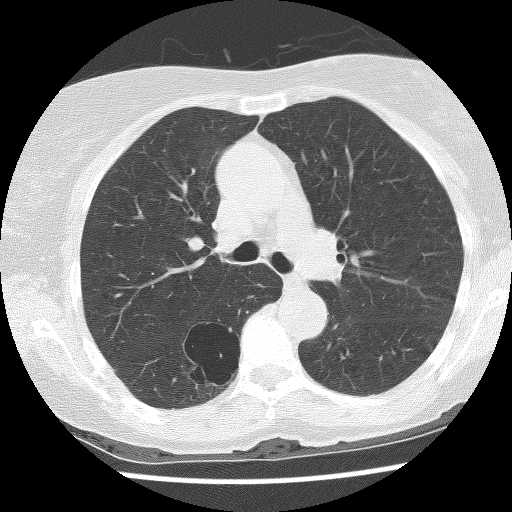
Low-dose screening chest CT, axial slice; baseline annual screen; lung window (W 1500 / L -600 HU); lung (sharp) reconstruction kernel (BONE); 512 × 512 image matrix. Female, age 69 years at enrolment. Former smoker at enrolment.
- Expert reader's lesion annotation, box from (x=166, y=322) to (x=245, y=396) px.
- The screening reader recorded 2 non-calcified nodules or masses ≥4 mm on this exam (right lower lobe, right lower lobe); which of them this box marks is not recorded.
- Official screen result: positive, change unspecified: nodule(s) >= 4 mm or enlarging nodule(s), mass(es), or other non-specific abnormalities suspicious for lung cancer.
- Participant outcome: lung cancer diagnosed 288 days after this screen — non-small cell carcinoma, right lower lobe, poorly differentiated (G3), stage IB (AJCC 6th edition), 36 mm at pathology.